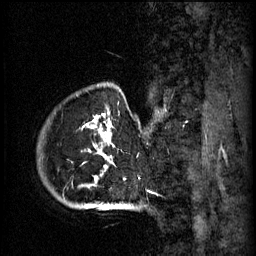
Breast MRI (dynamic contrast-enhanced), one sagittal slice; position 54 of 60 along the scan axis; 3 images stored at this slice position (order not interpretable as contrast timing); 1.5 T; TE 4.2 ms, TR 11 ms; 2 mm slice thickness; 256 × 256 image matrix, field of view 200 × 200 mm. Patient: female, 51 years.
Structures marked on this image (semi-automatically segmented with operator editing):
- analysis volume of interest (the breast-tissue region the enhancement analysis was run in; not a lesion): bounding box <48,84,161,197> (left, top, right, bottom; pixels)
- tumour enhancement mask (voxels above the 70 % enhancement threshold inside the analysis volume of interest): <84,114,113,187>